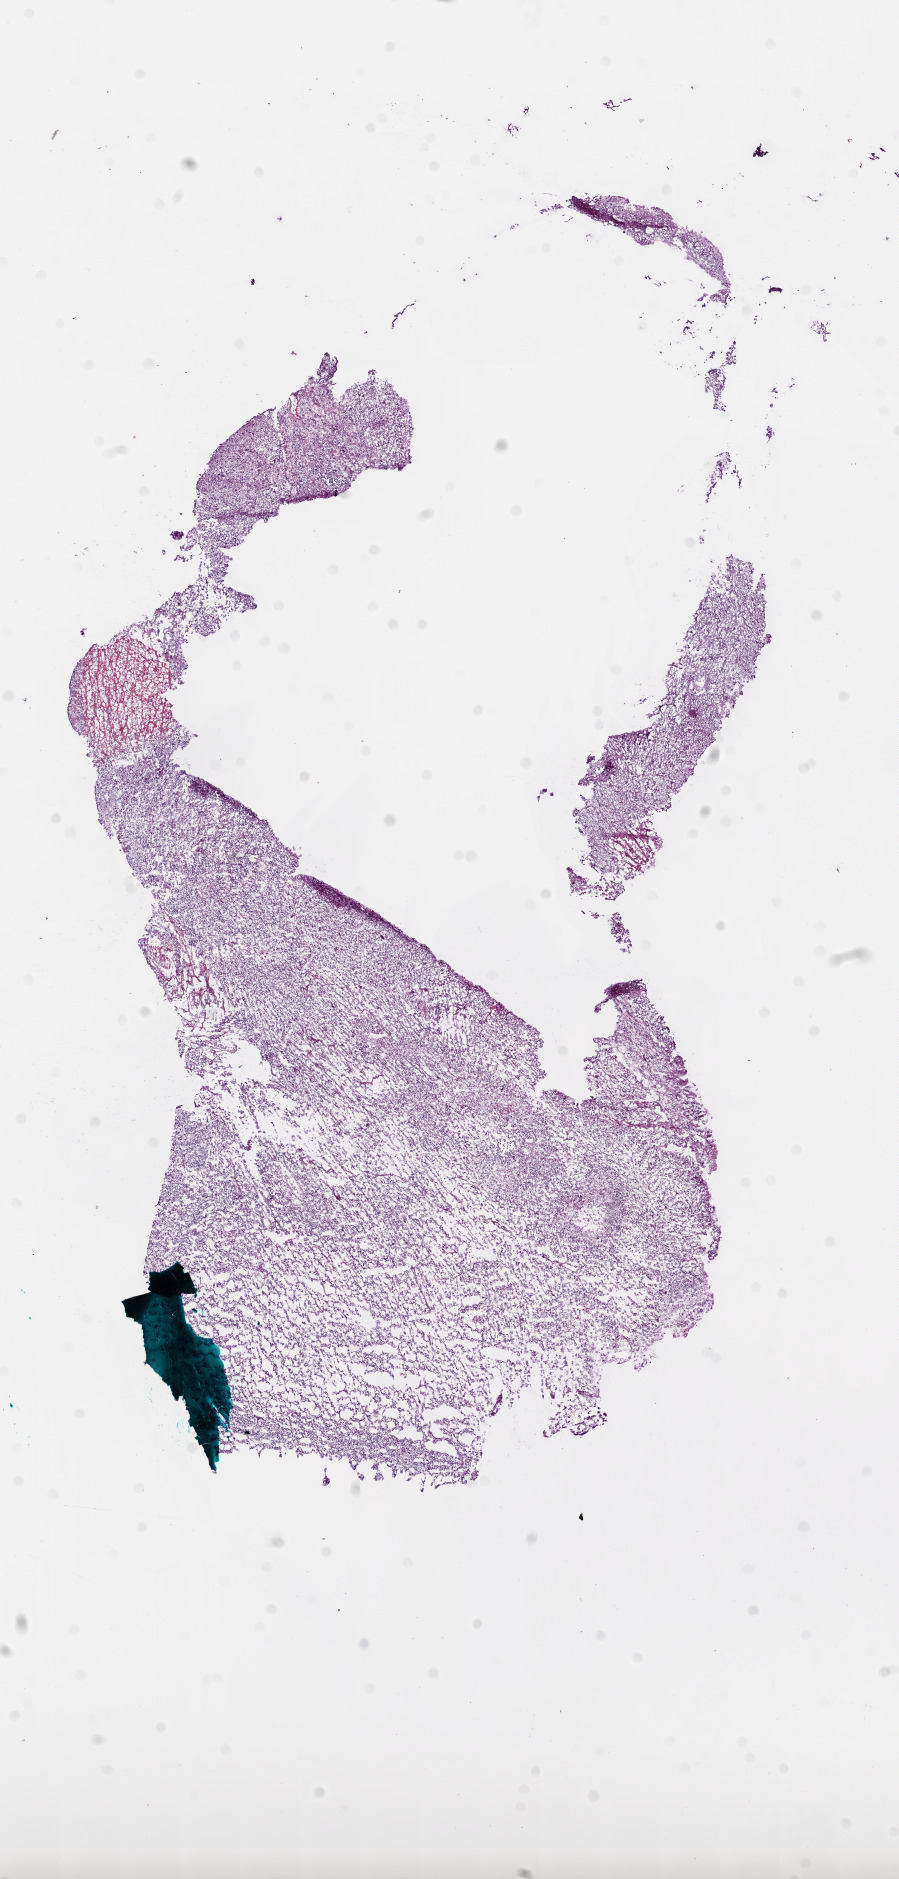
H&E-stained whole-slide image — a low-resolution overview of the entire scanned area, about 7.3 x 15.2 mm, frozen section from the bottom of the tissue portion, sample: primary tumour, brain. Patient: female, age at initial diagnosis 65 years. Pathologist review of this section (percent, as recorded): tumour cells 80%, tumour nuclei 90%, stromal cells 10%, necrosis 10%.
Diagnosis: Glioblastoma.